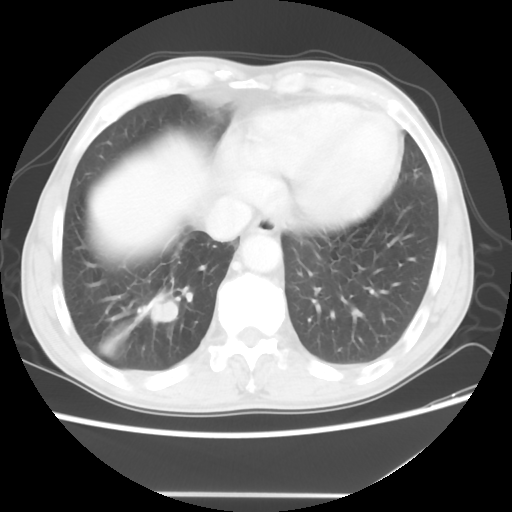
Chest CT, one axial slice. Slice 13 of 56 in the series (ordered by position). Lung window (W 1500 / L -600 HU). 512 × 512 image matrix, field of view 344 × 344 mm. Patient: male, 65 years. Case-level facts recorded for this patient, not image findings: clinical TNM (as recorded): T1c N3 M0.
Annotated regions visible in this slice (bounding box drawn by a radiologist):
- lung tumour (recorded histology: small cell carcinoma): box from (x=134, y=290) to (x=189, y=324) px